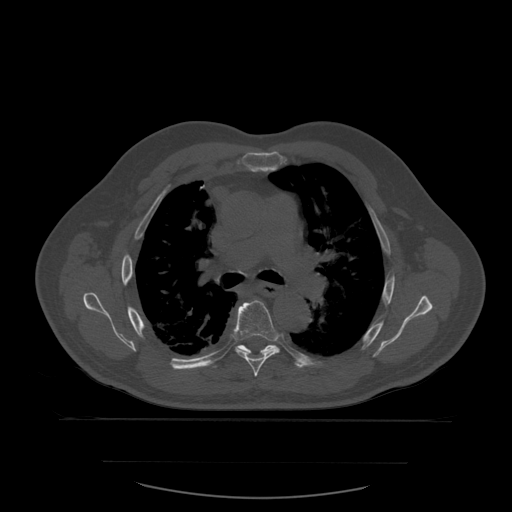
CT including the spine, one axial slice; slice 399 of 590 in the series (ordered by position); bone window (W 1800 / L 400 HU); 1.25 mm slice thickness; 512 × 512 image matrix. Patient age 71 years. From the clinical record (not read from this slice): primary cancer: lung; vertebrae with lytic lesions (as recorded): T1, T2, L5, S1.
Structures marked on this image (semi-automatic segmentation, software-assisted and operator-edited):
- T6 vertebra: bounding box <234,300,281,377> (left, top, right, bottom; pixels)
- T7 vertebra: <236,345,280,353>